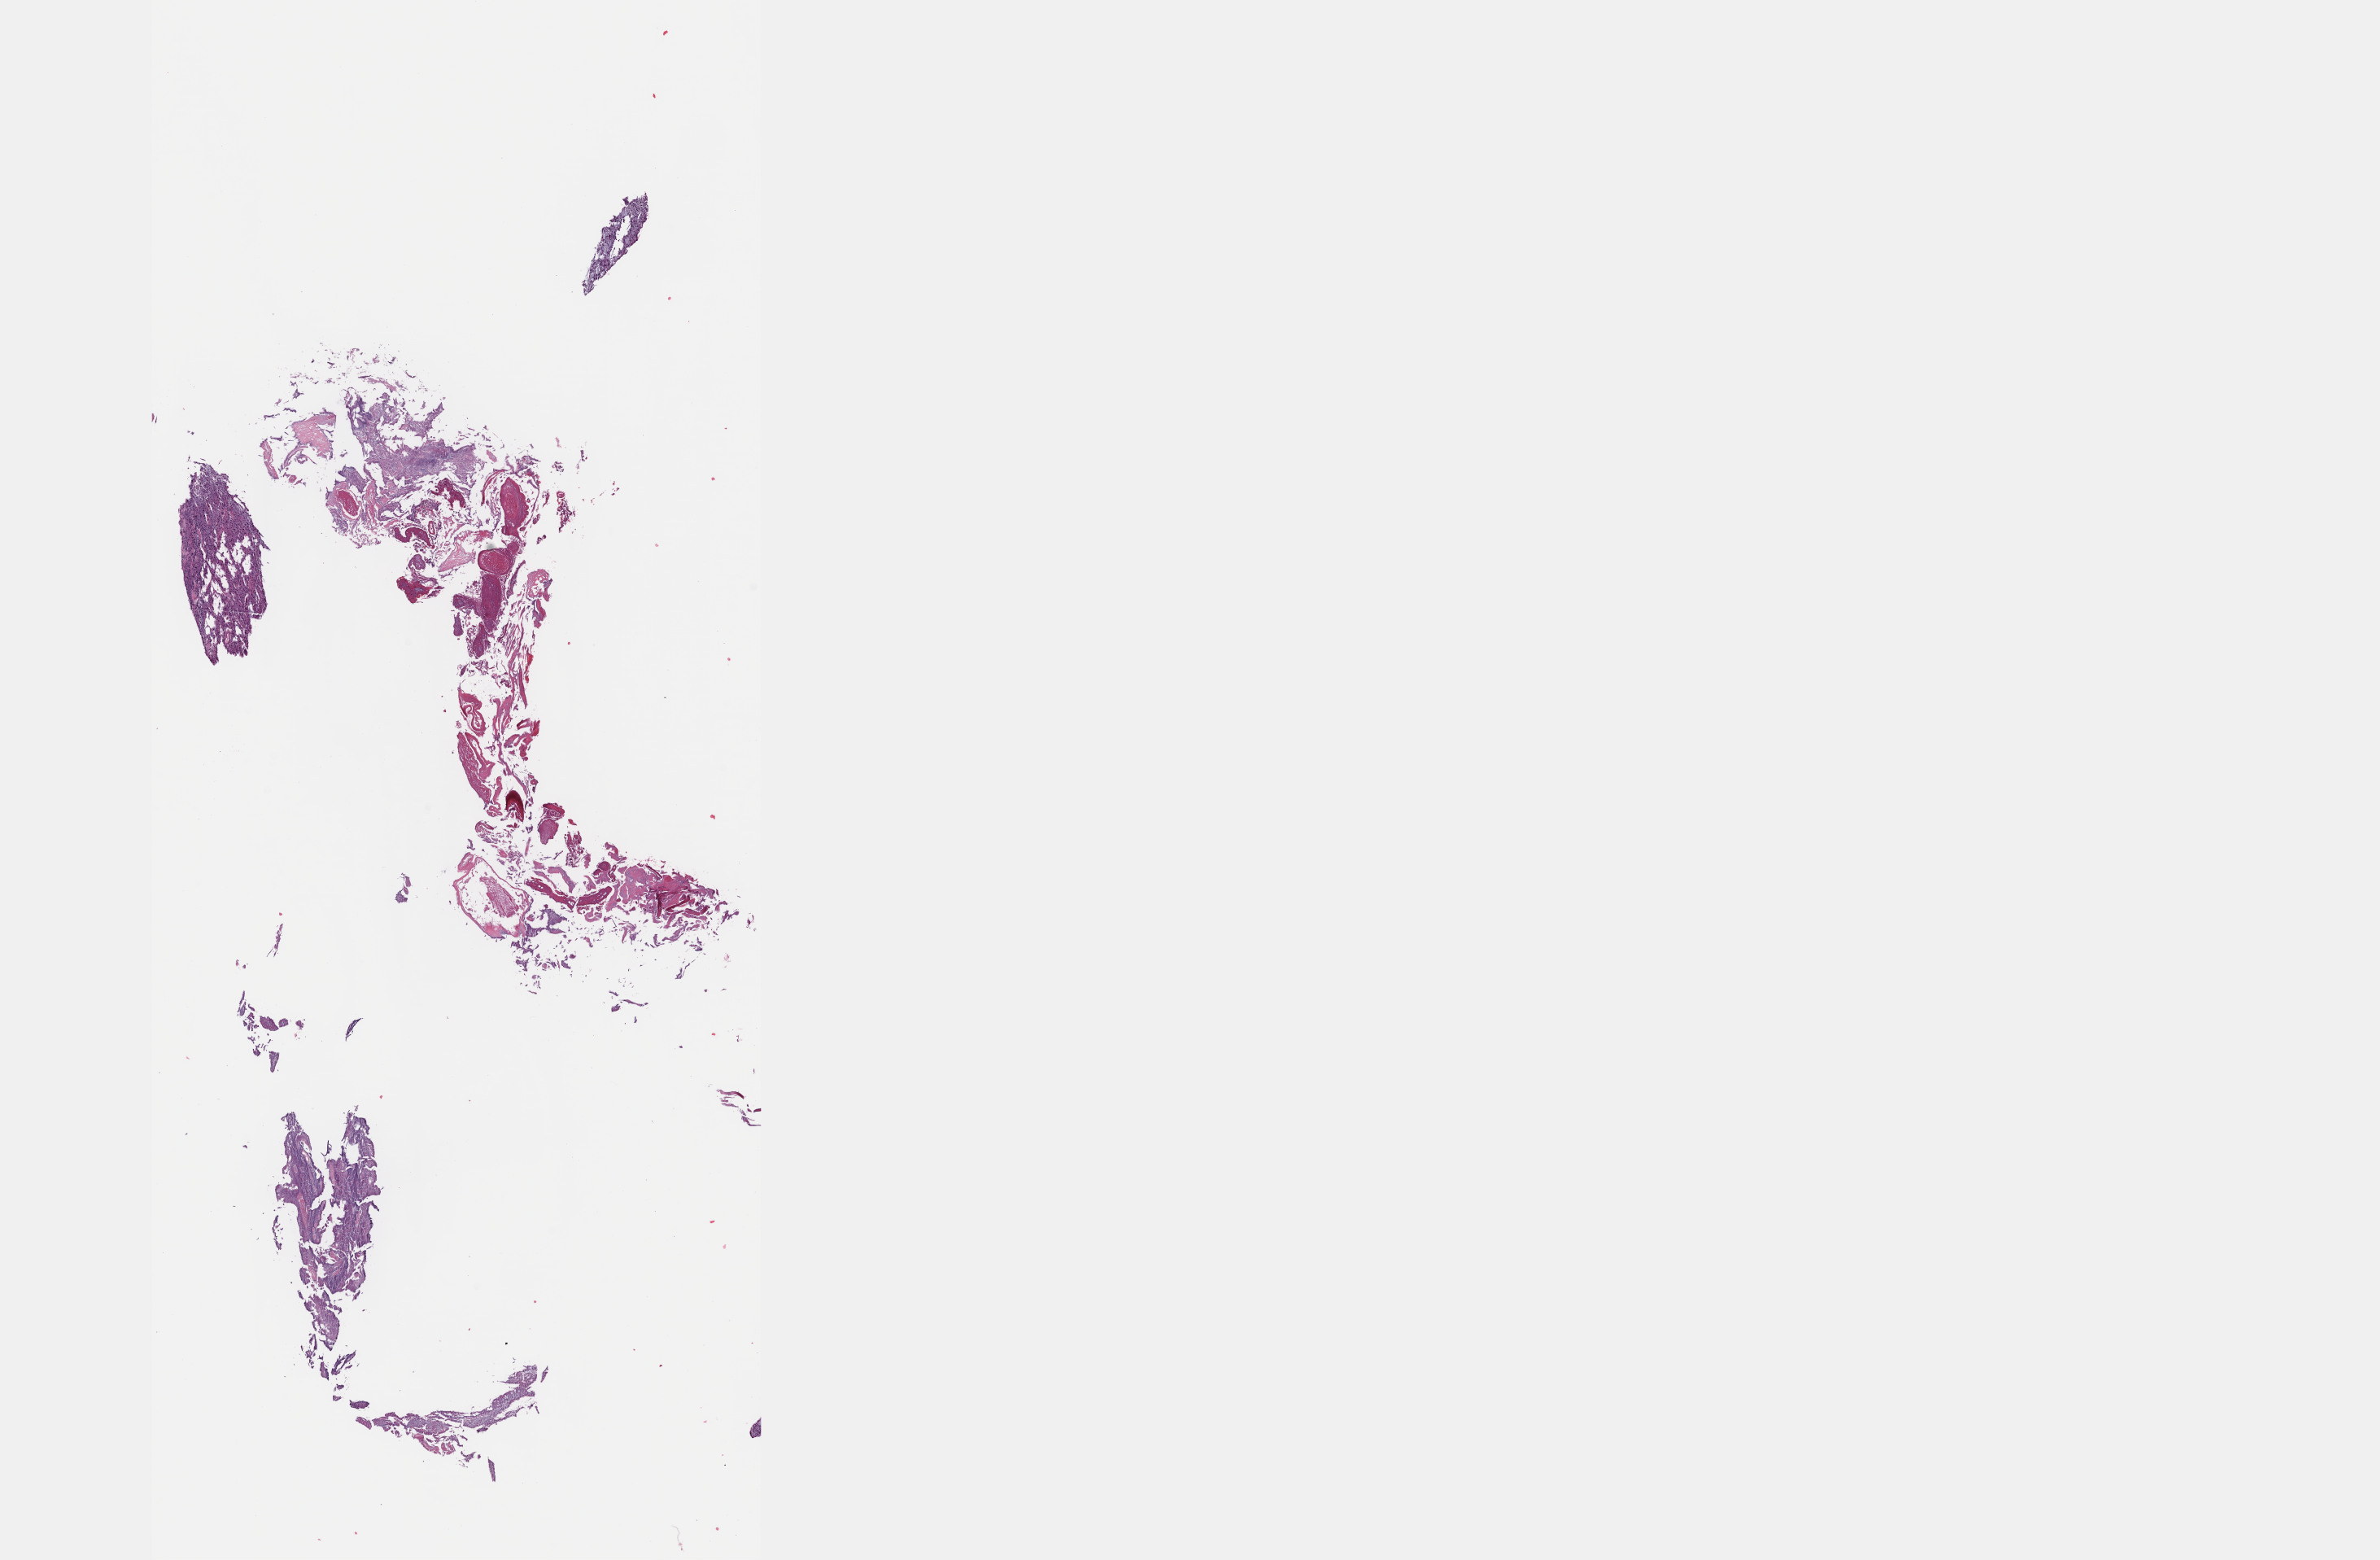
H&E-stained whole-slide image, low-resolution overview of the scanned area, about 23.6 x 15.5 mm (from a 40x scan); FFPE section; sample: primary tumour, brain. Patient: female, age at initial diagnosis 51 years. Histologic grade: G2 (moderately differentiated).
Histologic diagnosis: Oligodendroglioma, NOS.